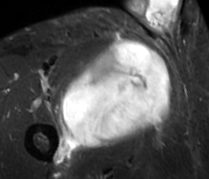
MRI of an extremity soft-tissue mass, one axial slice; STIR; MR volume resampled by the dataset authors to the PET/CT grid (not the native acquisition matrix); 3.27 mm slice thickness; 209 × 179 image matrix, field of view 204 × 175 mm. Male patient. Case-level facts recorded for this patient, not image findings: histological type: undifferentiated - pleiomorphic; grade: high; site of the primary tumour: right thigh.
Outlined on this slice (expert contour drawn on MRI and transferred to this co-registered scan by the dataset authors):
- gross tumour volume including surrounding oedema: box from (x=57, y=41) to (x=170, y=149) px
- gross tumour volume (mass): (x=60, y=41)–(x=170, y=149)